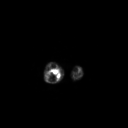
FDG PET of an extremity soft-tissue mass (from a PET/CT study), one axial slice. Position 72 of 267 along the scan axis. 3.27 mm slice thickness. 128 × 128 image matrix, field of view 700 × 700 mm. Patient: male, 34 years. From the clinical record (not read from this slice): histological type: liposarcoma - round cell; grade: high; site of the primary tumour: right calf.
Outlined on this slice (expert contour drawn on MRI and transferred to this co-registered scan by the dataset authors):
- gross tumour volume (mass): bounding box <46,67,62,84> (left, top, right, bottom; pixels)